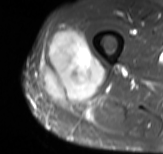
MRI of an extremity soft-tissue mass, one axial slice; position 35 of 61 along the scan axis; STIR; MR volume resampled by the dataset authors to the PET/CT grid (not the native acquisition matrix); 3.27 mm slice thickness; 163 × 154 image matrix, field of view 159 × 150 mm. Male patient. Case-level facts recorded for this patient, not image findings: histological type: poorly differentiated synovial sarcoma; grade: high; site of the primary tumour: right buttock.
Annotated regions visible in this slice (expert contour drawn on MRI and transferred to this co-registered scan by the dataset authors):
- gross tumour volume including surrounding oedema: box from (x=41, y=30) to (x=104, y=106) px
- gross tumour volume (mass): (x=43, y=30)–(x=104, y=106)